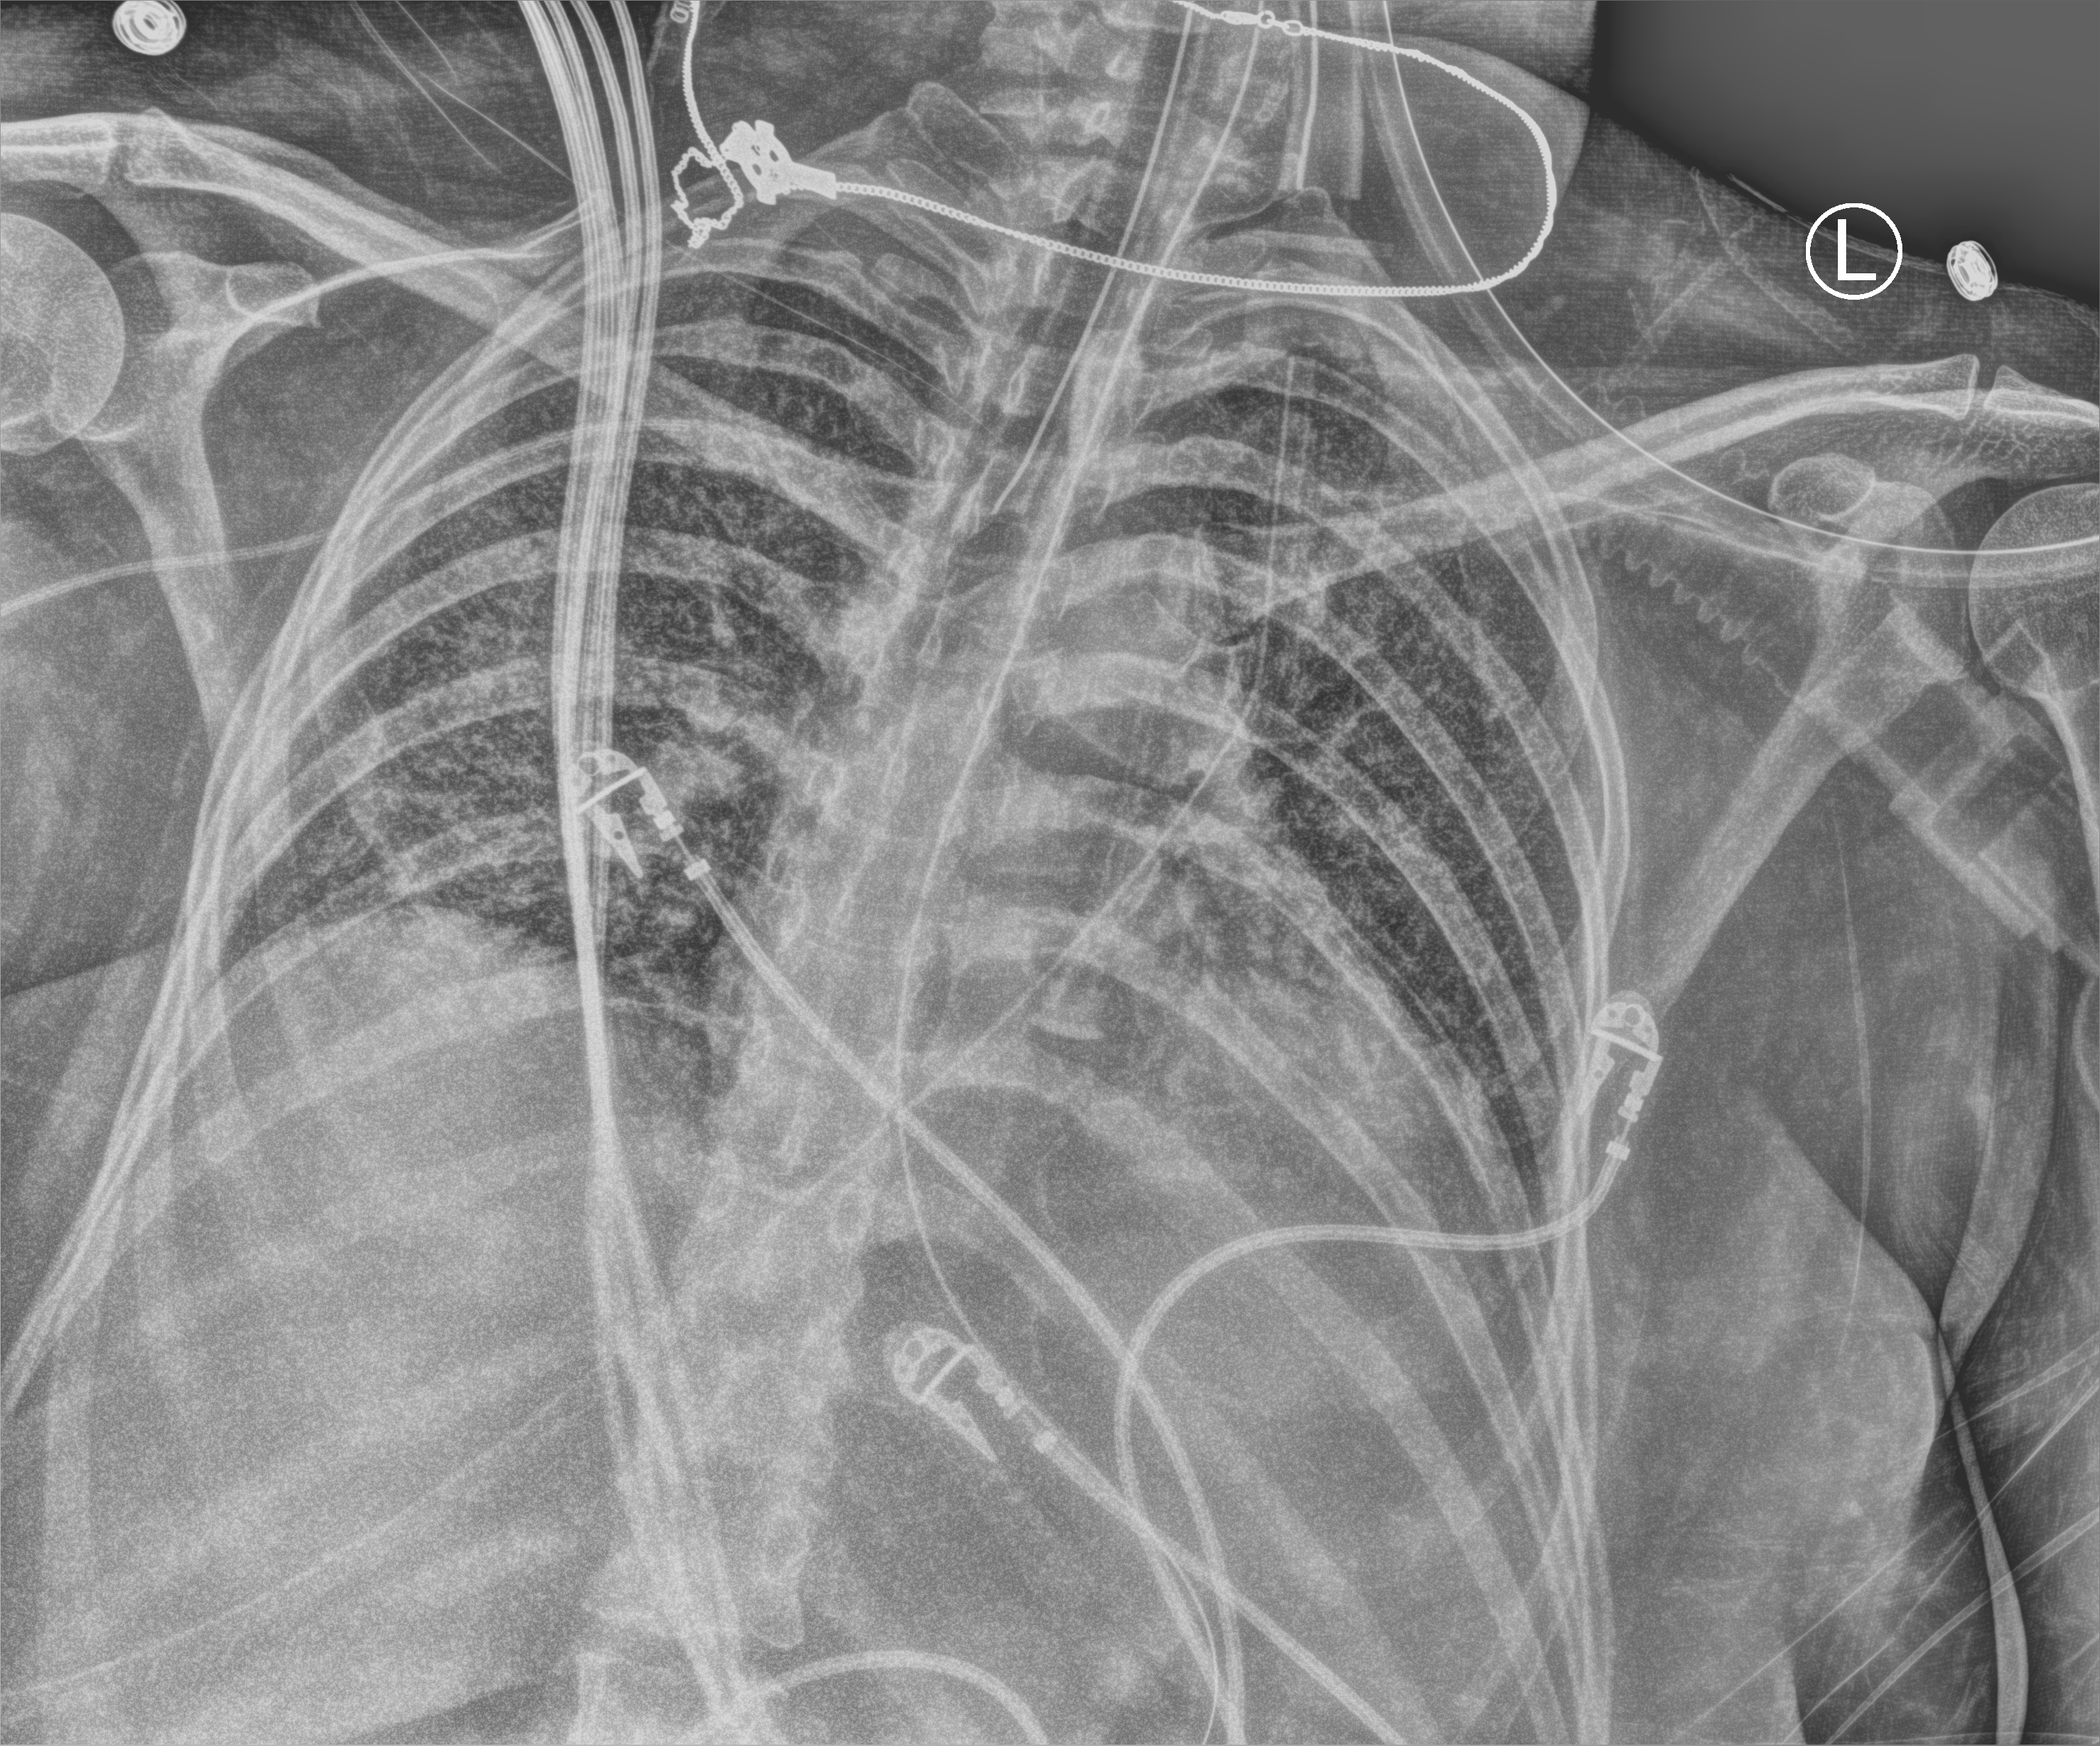
Chest X-ray (portable), anteroposterior (AP) projection. Female patient hospitalised with COVID-19, age 18–59 years.
Hospital-stay facts (about this admission, not read from this image; timing relative to this image not recorded):
- admitted to intensive care during this hospital stay: yes
- length of hospital stay: 73 days